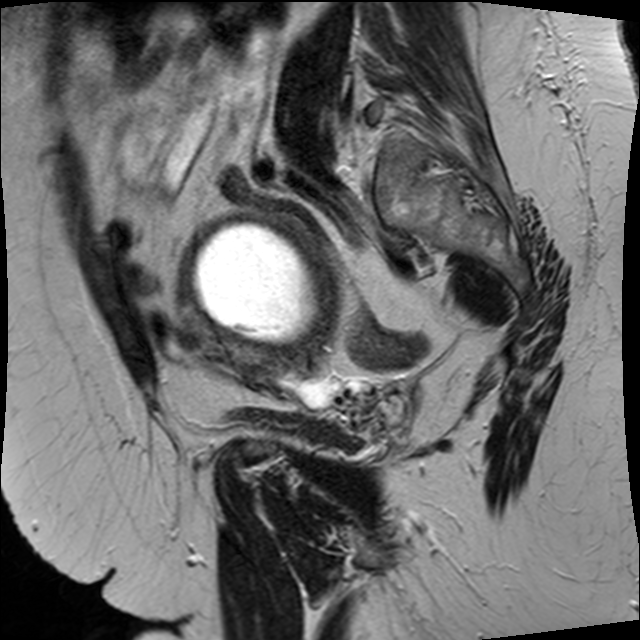
Pelvic MRI for cervical cancer, one sagittal slice. Slice 25 of 34 in the series (ordered by position). T2-weighted. 1.5 T. TE 89 ms, TR 3320 ms. 640 × 640 image matrix, field of view 260 × 260 mm. Patient: female, 50 years.
Annotated regions visible in this slice (expert manual segmentation):
- uterus and cervix: bounding box (x1, y1, x2, y2) in pixels: (175, 212, 337, 362)